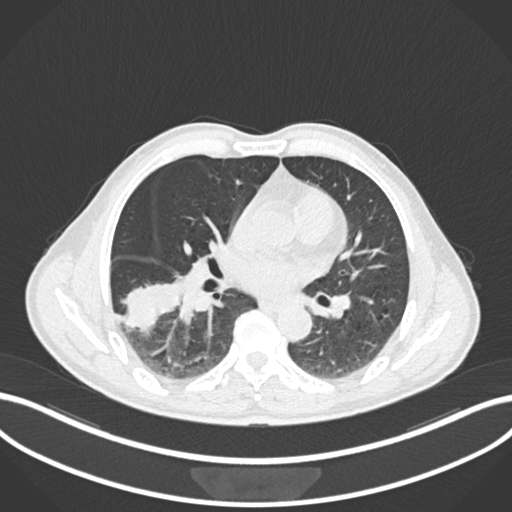
Chest CT, one axial slice; slice 96 of 208 in the series (ordered by position); 120 kVp; lung window (W 1500 / L -600 HU); 1 mm slice thickness; 512 × 512 image matrix, field of view 400 × 400 mm. Patient: male, 58 years. Case-level facts recorded for this patient, not image findings: clinical TNM (as recorded): T3 N0 M0.
Annotated regions visible in this slice (rectangle marked by the reading radiologist):
- lung tumour (recorded histology: squamous cell carcinoma): bounding box (x1, y1, x2, y2) in pixels: (119, 269, 183, 335)